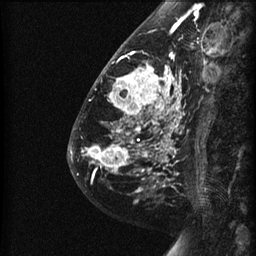
Breast MRI (dynamic contrast-enhanced), one sagittal slice. Position 21 of 60 along the scan axis. Dynamic contrast-enhanced series, image 2 of 3 at this slice position (ordered by acquisition). 1.5 T. TE 4.2 ms, TR 22.7 ms. 256 × 256 image matrix, field of view 180 × 180 mm. Female patient, age 48 years. Case-level facts recorded for this patient, not image findings: setting: breast cancer imaged before/during neoadjuvant chemotherapy; receptor status: triple-negative.
Outlined on this slice (semi-automatic segmentation, software-assisted and operator-edited):
- analysis volume of interest (the breast-tissue region the enhancement analysis was run in; not a lesion): bounding box [x1, y1, x2, y2] px = [89, 27, 191, 180]
- tumour enhancement mask (voxels above the 90 % enhancement threshold inside the analysis volume of interest): [89, 27, 182, 172]